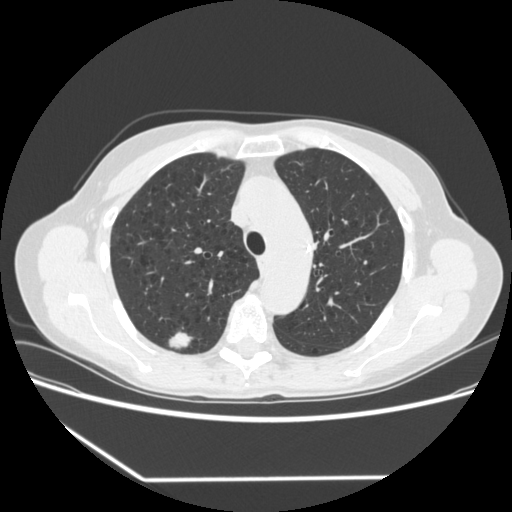
Axial slice from a low-dose chest CT screening exam; baseline screening round; lung window (W 1500 / L -600 HU); 1.25 mm slice thickness; standard (soft-tissue) reconstruction kernel (STANDARD); 120 kVp. Female, age 67 years at enrolment. Current smoker at enrolment.
Expert reader's lesion annotation, bounding box (x1, y1, x2, y2) in pixels: (154, 322, 199, 357). The screening reader recorded 2 non-calcified nodules or masses ≥4 mm on this exam; which of them this box marks is not recorded. Official screen result: positive, change unspecified: nodule(s) >= 4 mm or enlarging nodule(s), mass(es), or other non-specific abnormalities suspicious for lung cancer. Lung cancer was diagnosed 29 days after this screen: adenocarcinoma, NOS, right upper lobe, moderately differentiated (G2), stage IA (AJCC 6th edition), 24 mm at pathology.